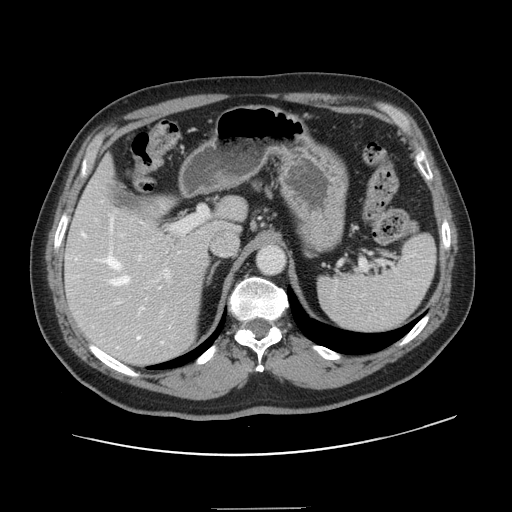
Contrast-enhanced abdominal CT, one axial slice. Slice 93 of 143 in the series (ordered by position). Soft-tissue window (W 400 / L 40 HU). 2.5 mm slice thickness. 512 × 512 image matrix, field of view 402 × 402 mm. Male patient, age 62 years. Case-level facts recorded for this patient, not image findings: diagnosis: colorectal cancer liver metastases, imaged before liver resection; multiple liver metastases: yes; largest metastasis: 2.7 cm; disease in both lobes: no.
Outlined on this slice (manually delineated by an expert):
- hepatic veins: bounding box (x1, y1, x2, y2) in pixels: (82, 217, 163, 348)
- liver: (66, 163, 245, 364)
- planned liver remnant (the part of the liver to remain after resection): (69, 162, 244, 251)
- portal vein (with intrahepatic branches): (76, 206, 208, 305)